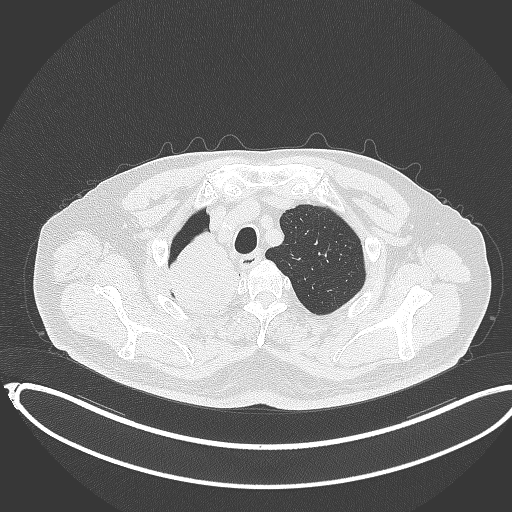
Chest CT, one axial slice. Position 317 of 403 along the scan axis. Reconstruction kernel B70f. 120 kVp. Lung window (W 1500 / L -600 HU). 1 mm slice thickness. 512 × 512 image matrix. Patient: male, 68 years. From the clinical record (not read from this slice): clinical TNM (as recorded): T2a N0 M0.
Structures marked on this image (rectangle marked by the reading radiologist):
- lung tumour (recorded histology: adenocarcinoma): bounding box [x1, y1, x2, y2] px = [167, 233, 250, 313]